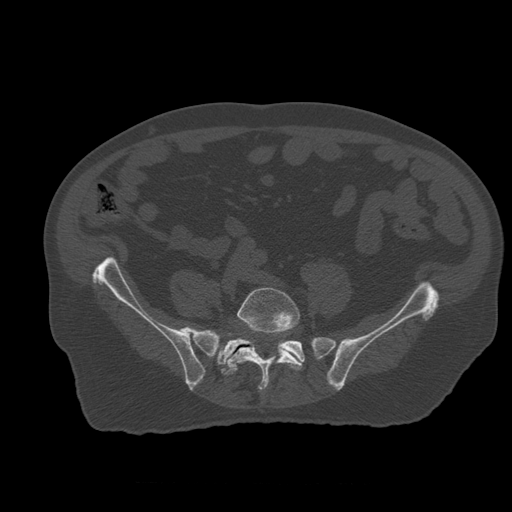
CT including the spine, one axial slice. Position 135 of 399 along the scan axis. 120 kVp. Bone window (W 1800 / L 400 HU). 1.25 mm slice thickness. 512 × 512 image matrix, field of view 407 × 407 mm. Patient age 73 years. From the clinical record (not read from this slice): primary cancer: prostate; vertebrae with lytic lesions (as recorded): L2.
Structures marked on this image (semi-automatic segmentation, software-assisted and operator-edited):
- L5 vertebra: bounding box (x1, y1, x2, y2) in pixels: (222, 288, 303, 391)